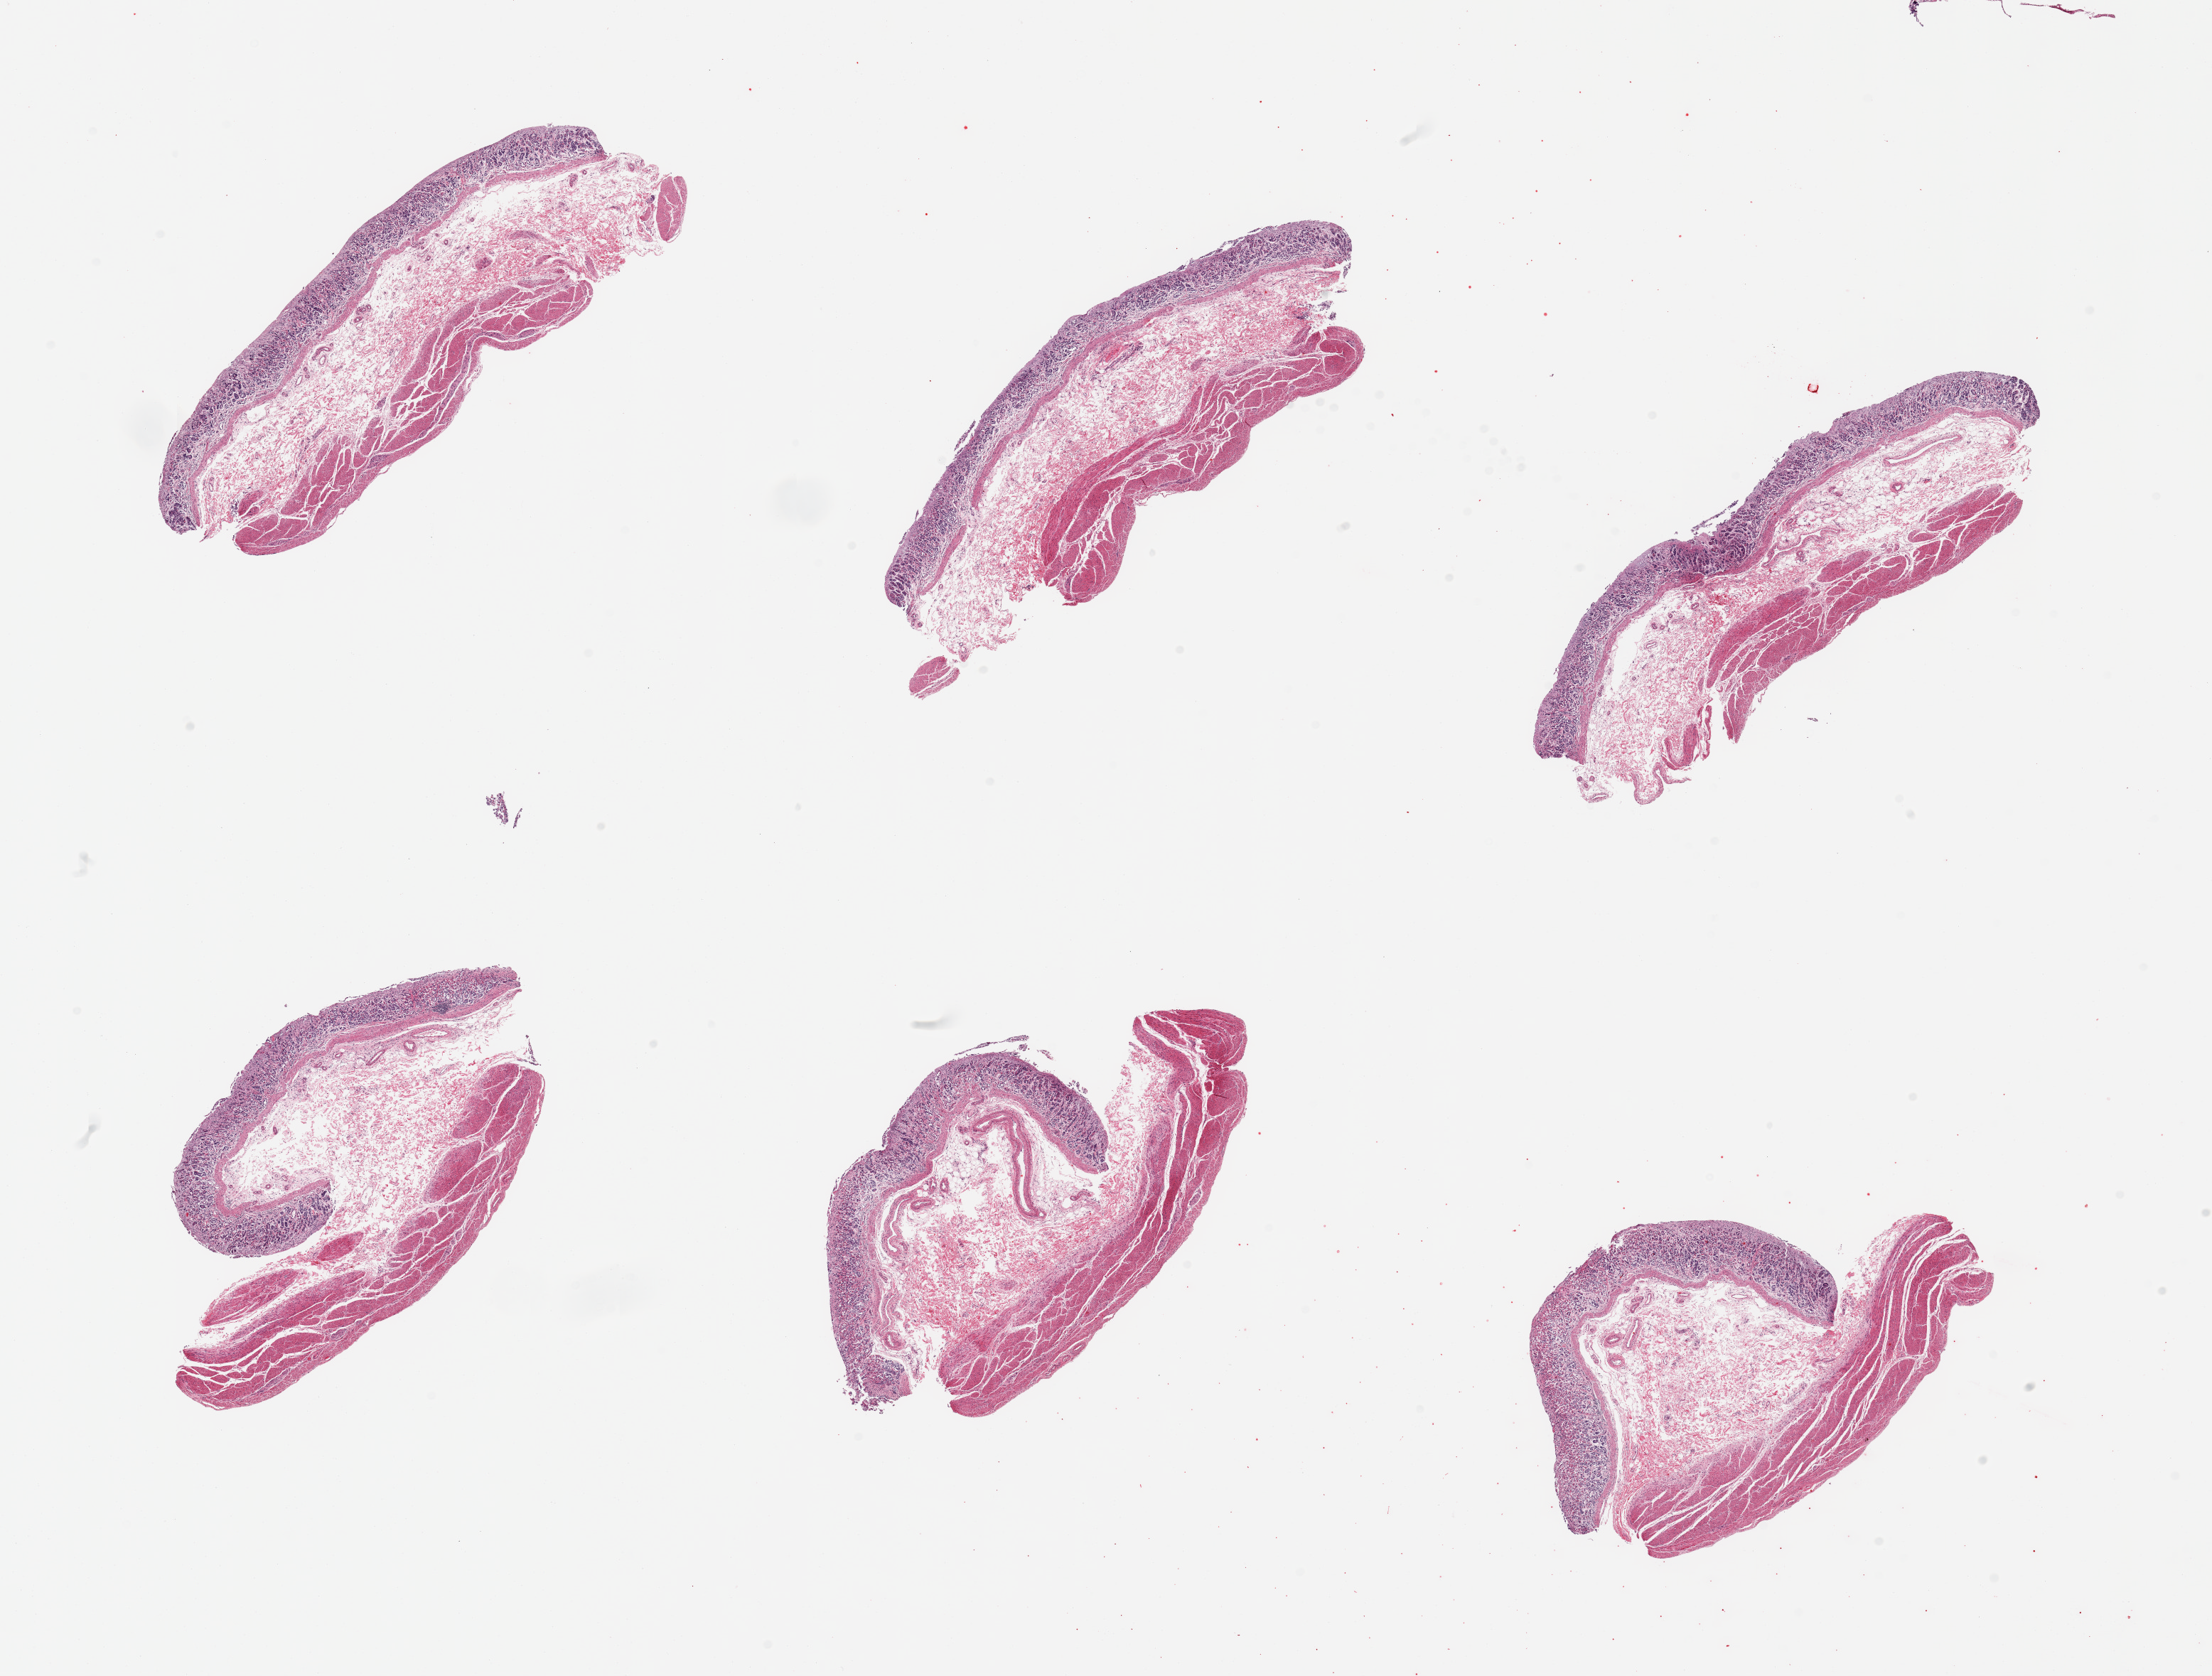
Whole-slide image, hematoxylin and eosin (H&E) stain — a low-resolution overview of the entire scanned area, about 24.6 x 18.6 mm (from a 20x scan). PAXgene-fixed paraffin-embedded (PFPE) section. Target tissue: stomach. Donor tissue sample. Male donor.
- review note (as recorded): 6 pieces; mucosa autolyzed, muscle intact